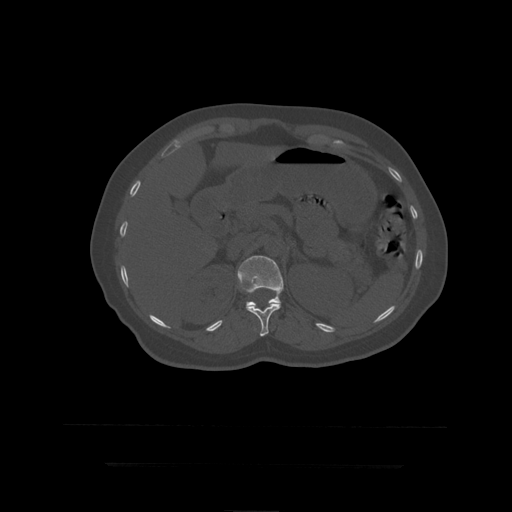
CT including the spine, one axial slice. Slice 187 of 399 in the series (ordered by position). 120 kVp. Bone window (W 1800 / L 400 HU). 512 × 512 image matrix, field of view 450 × 450 mm. Patient age 41 years. From the clinical record (not read from this slice): primary cancer: breast.
Structures marked on this image (semi-automatic segmentation, software-assisted and operator-edited):
- L1 vertebra: bounding box (x1, y1, x2, y2) in pixels: (238, 256, 284, 308)
- T12 vertebra: (246, 303, 281, 337)